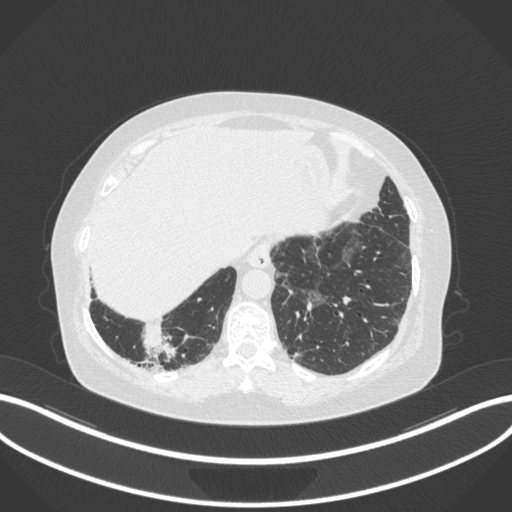
Chest CT, one axial slice; slice 23 of 303 in the series (ordered by position); reconstruction kernel B31f; lung window (W 1500 / L -600 HU); 1 mm slice thickness; 512 × 512 image matrix, field of view 400 × 400 mm. Patient: female, 65 years. From the clinical record (not read from this slice): clinical TNM (as recorded): T2b N1 M0; histopathological grade: G1.
Outlined on this slice (rectangle marked by the reading radiologist):
- lung tumour (recorded histology: adenocarcinoma): box from (x=139, y=320) to (x=178, y=363) px